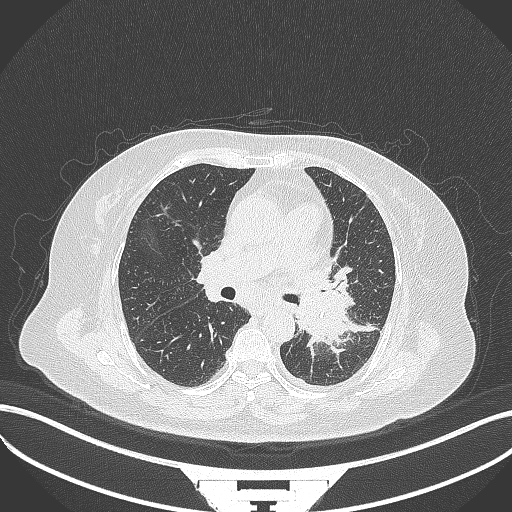
Chest CT, one axial slice; position 196 of 322 along the scan axis; reconstruction kernel B70f; lung window (W 1500 / L -600 HU); 512 × 512 image matrix. Female patient, age 69 years. Case-level facts recorded for this patient, not image findings: clinical TNM (as recorded): T2b N3 M1.
Structures marked on this image (rectangle marked by the reading radiologist):
- lung tumour (recorded histology: adenocarcinoma): bounding box <295,281,357,346> (left, top, right, bottom; pixels)